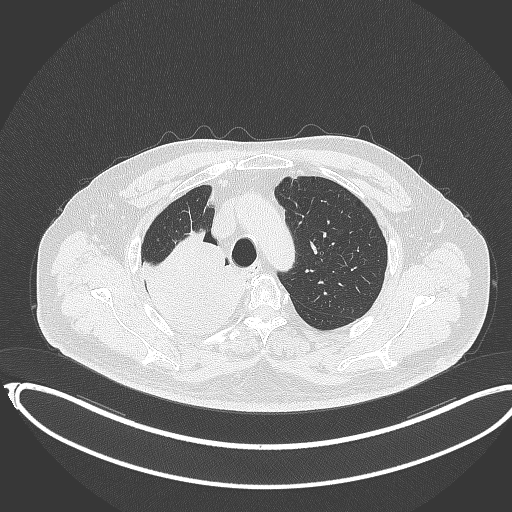
Chest CT, one axial slice; position 285 of 403 along the scan axis; reconstruction kernel B70f; 120 kVp; lung window (W 1500 / L -600 HU); 1 mm slice thickness; 512 × 512 image matrix, field of view 436 × 436 mm. Patient: male, 68 years. From the clinical record (not read from this slice): clinical TNM (as recorded): T2a N0 M0.
Annotated regions visible in this slice (rectangle marked by the reading radiologist):
- lung tumour (recorded histology: adenocarcinoma): bounding box (x1, y1, x2, y2) in pixels: (136, 229, 255, 335)